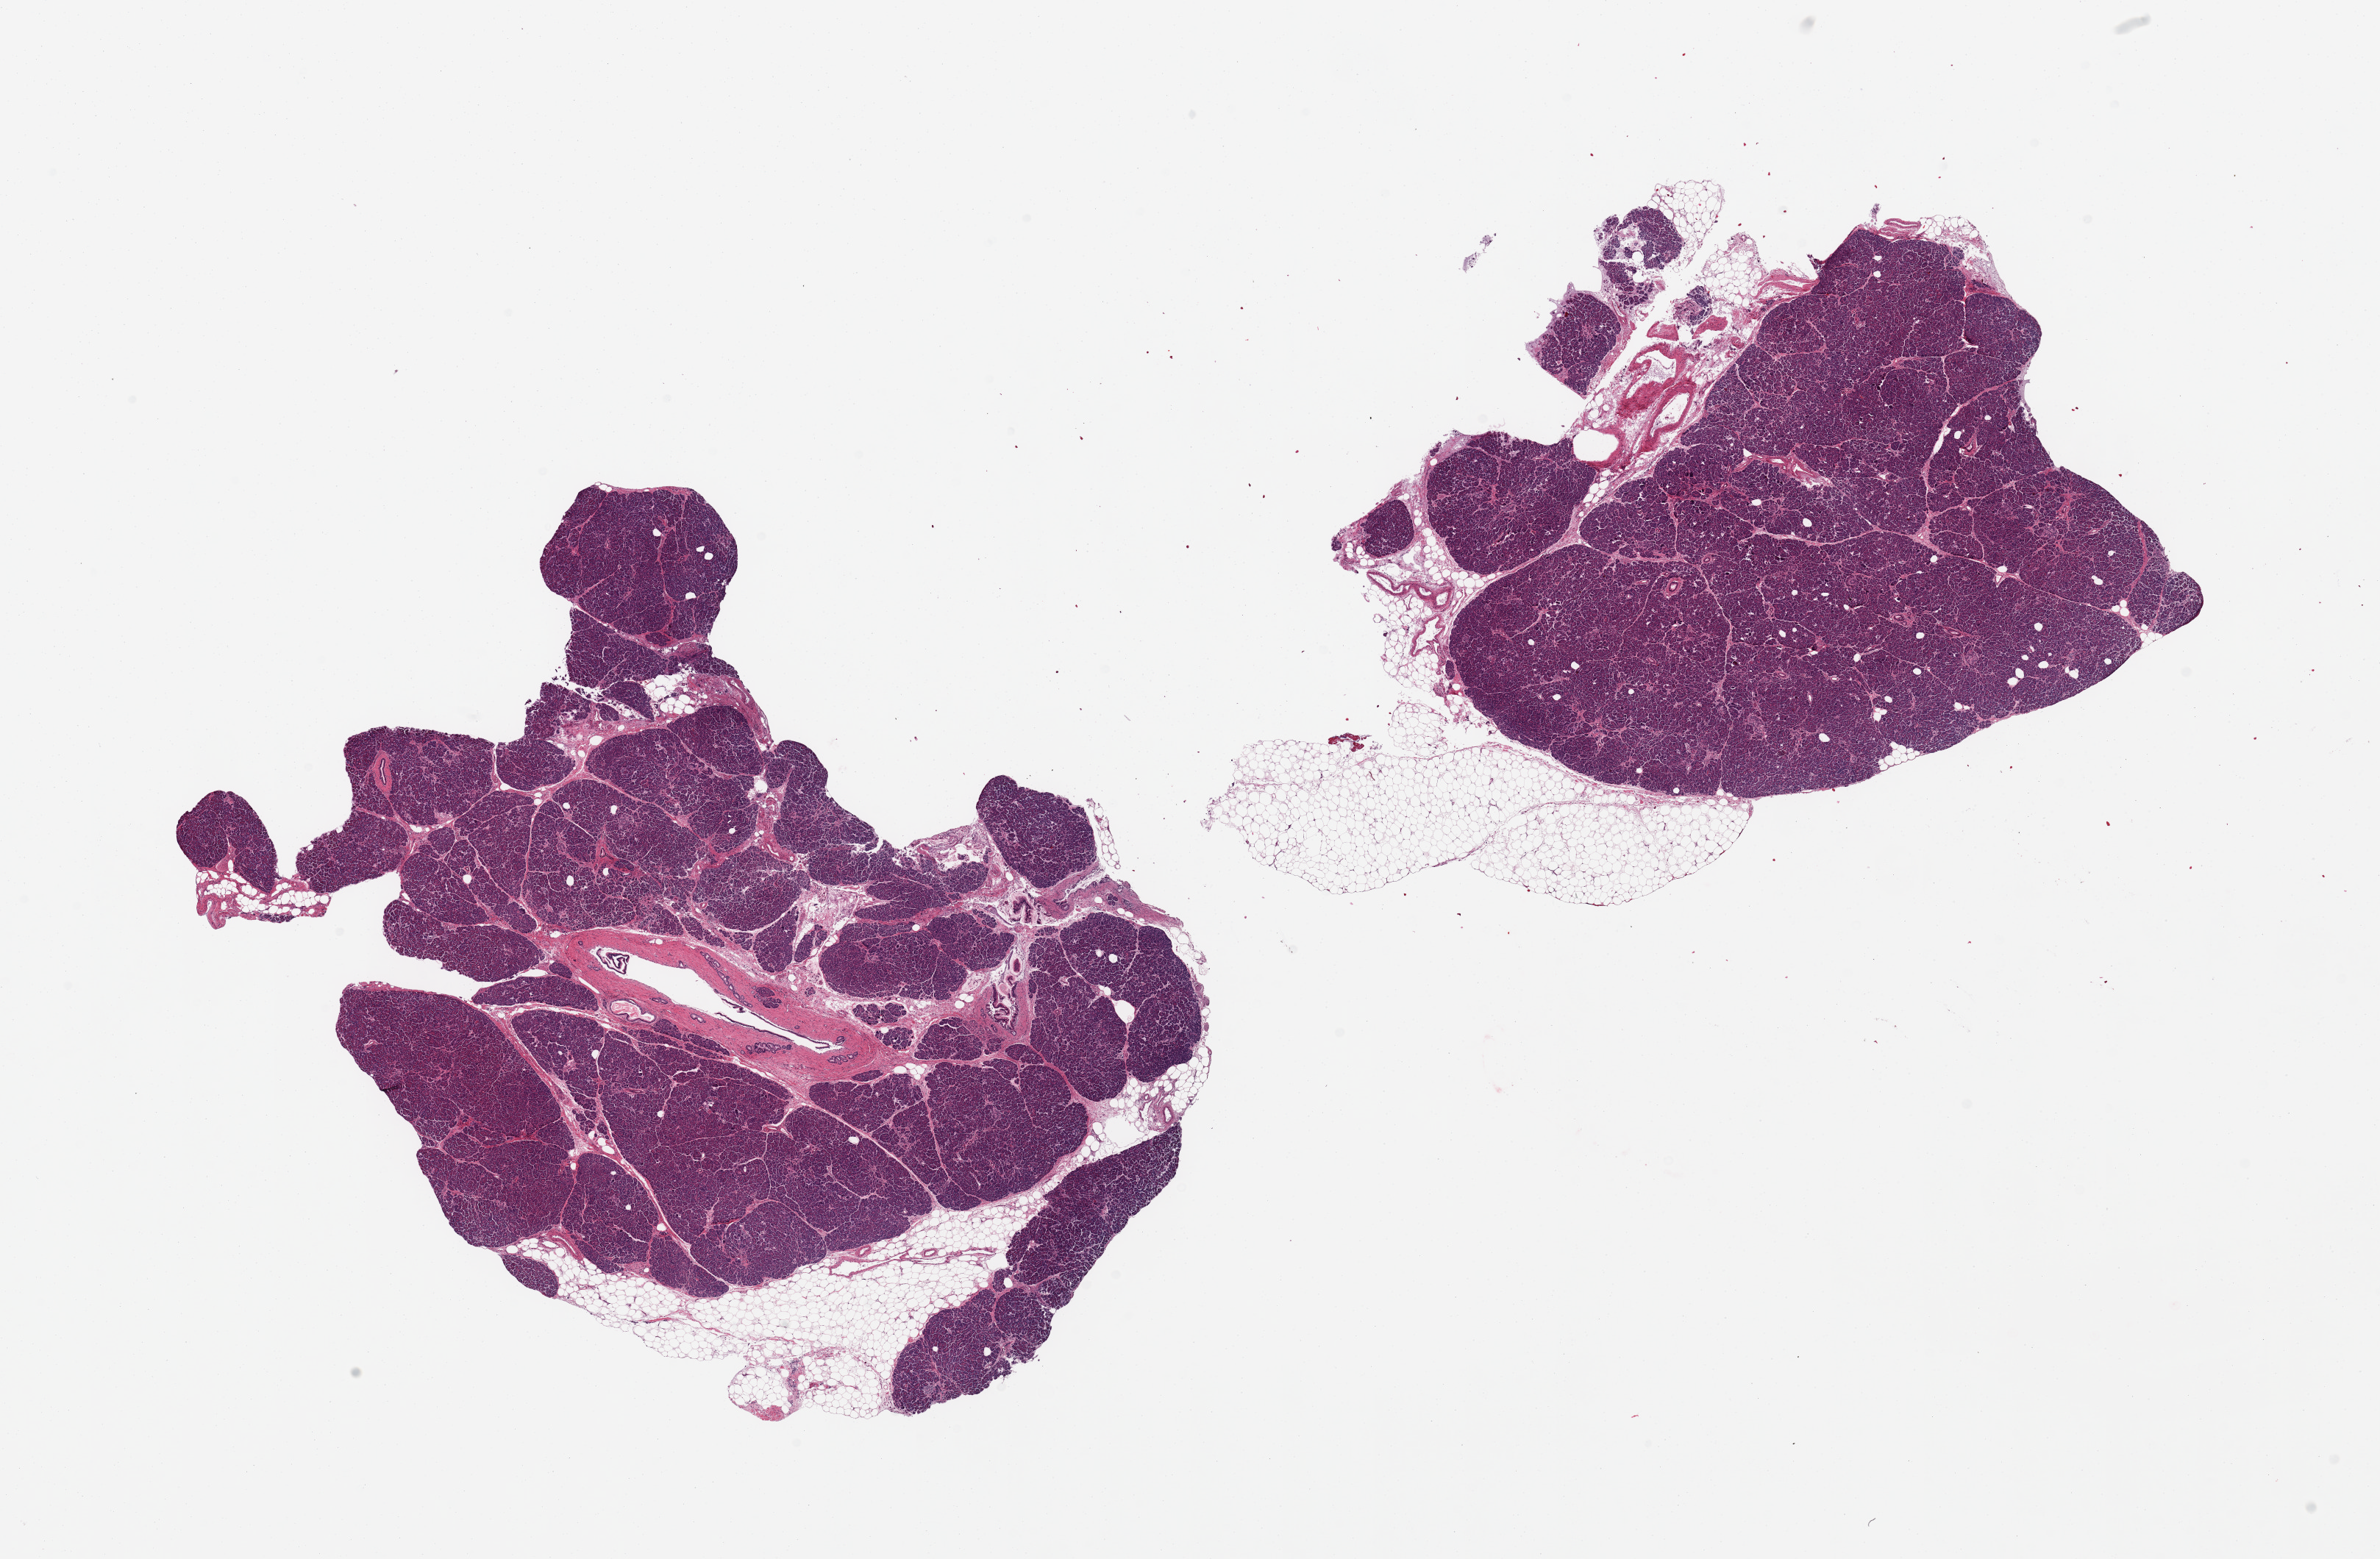
Haematoxylin and eosin whole-slide image — shown as a low-resolution overview of the whole scanned area (about 25.6 x 16.8 mm); PAXgene-fixed paraffin-embedded (PFPE) section; sampled site (target tissue): pancreas; tissue donor sample. Donor sex: female.
Reviewer comment on this tissue sample: 2 pieces, Islets rare but well preserved; Adherent fat is ~10-15%.